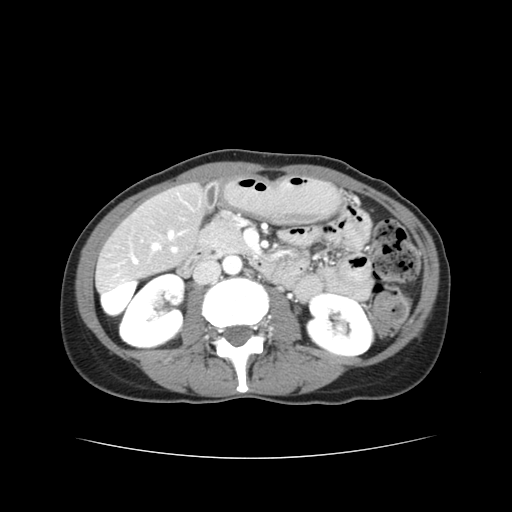
Contrast-enhanced abdominal CT, one axial slice; position 12 of 38 along the scan axis; reconstruction kernel STANDARD; 120 kVp; intravenous contrast given; soft-tissue window (W 400 / L 40 HU); 5 mm slice thickness; 512 × 512 image matrix. Female patient, age 54 years. From the clinical record (not read from this slice): diagnosis: colorectal cancer liver metastases, imaged before liver resection; multiple liver metastases: yes; largest metastasis: 1.1 cm; disease in both lobes: yes.
Annotated regions visible in this slice (outlined manually by an expert reader):
- hepatic veins: bounding box (x1, y1, x2, y2) in pixels: (153, 232, 174, 250)
- liver: (97, 185, 201, 286)
- portal vein (with intrahepatic branches): (133, 248, 176, 264)